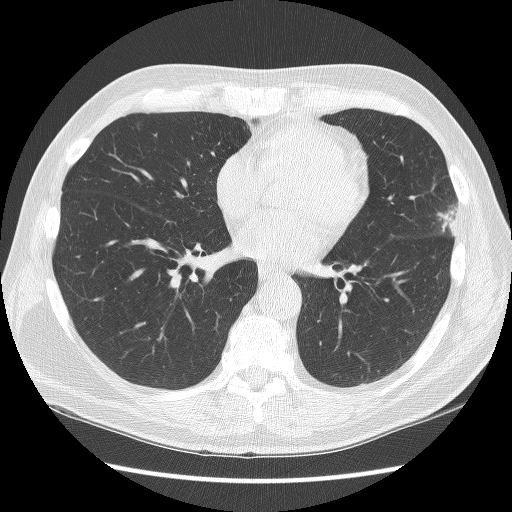
Chest CT (low-dose screening protocol), one axial image; third screening round (two years after baseline); lung window (W 1500 / L -600 HU); 2.5 mm slice thickness; lung (sharp) reconstruction kernel (BONE); slice 72 of 134 in the series; 512 × 512 image matrix. Male, age 67 years at enrolment.
Lesion marked by an expert reader, box from (x=409, y=184) to (x=472, y=257) px. The exam's reader record, not a measurement of the box and not confirmed to be the same lesion: non-calcified nodule or mass ≥4 mm, left upper lobe, 22 × 17 mm, poorly defined margins, soft tissue attenuation, pre-existing on the prior screen: yes; interval growth: yes. Lung cancer was diagnosed 72 days after this screen: squamous cell carcinoma, NOS, left upper lobe, moderately differentiated (G2), stage IB (AJCC 6th edition), 25 mm at pathology.